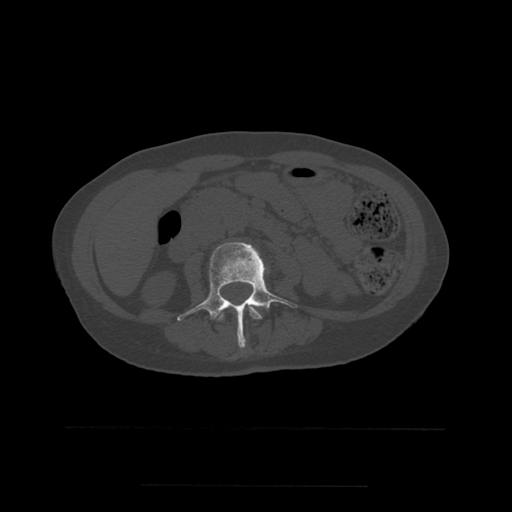
CT including the spine, one axial slice; bone window (W 1800 / L 400 HU); 512 × 512 image matrix, field of view 350 × 350 mm. Patient age 58 years. From the clinical record (not read from this slice): primary cancer: lung.
Annotated regions visible in this slice (semi-automatic segmentation, software-assisted and operator-edited):
- L2 vertebra: bounding box <219,306,263,321> (left, top, right, bottom; pixels)
- L3 vertebra: <177,242,298,349>